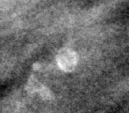
Cropped region of a digitized screen-film mammogram centred on a radiologist-marked abnormality, right breast, MLO view, BI-RADS breast density category 3 (scale 1–4).
Finding: calcifications, morphology lucent centered; BI-RADS assessment category 2; benign without callback (not worked up further).